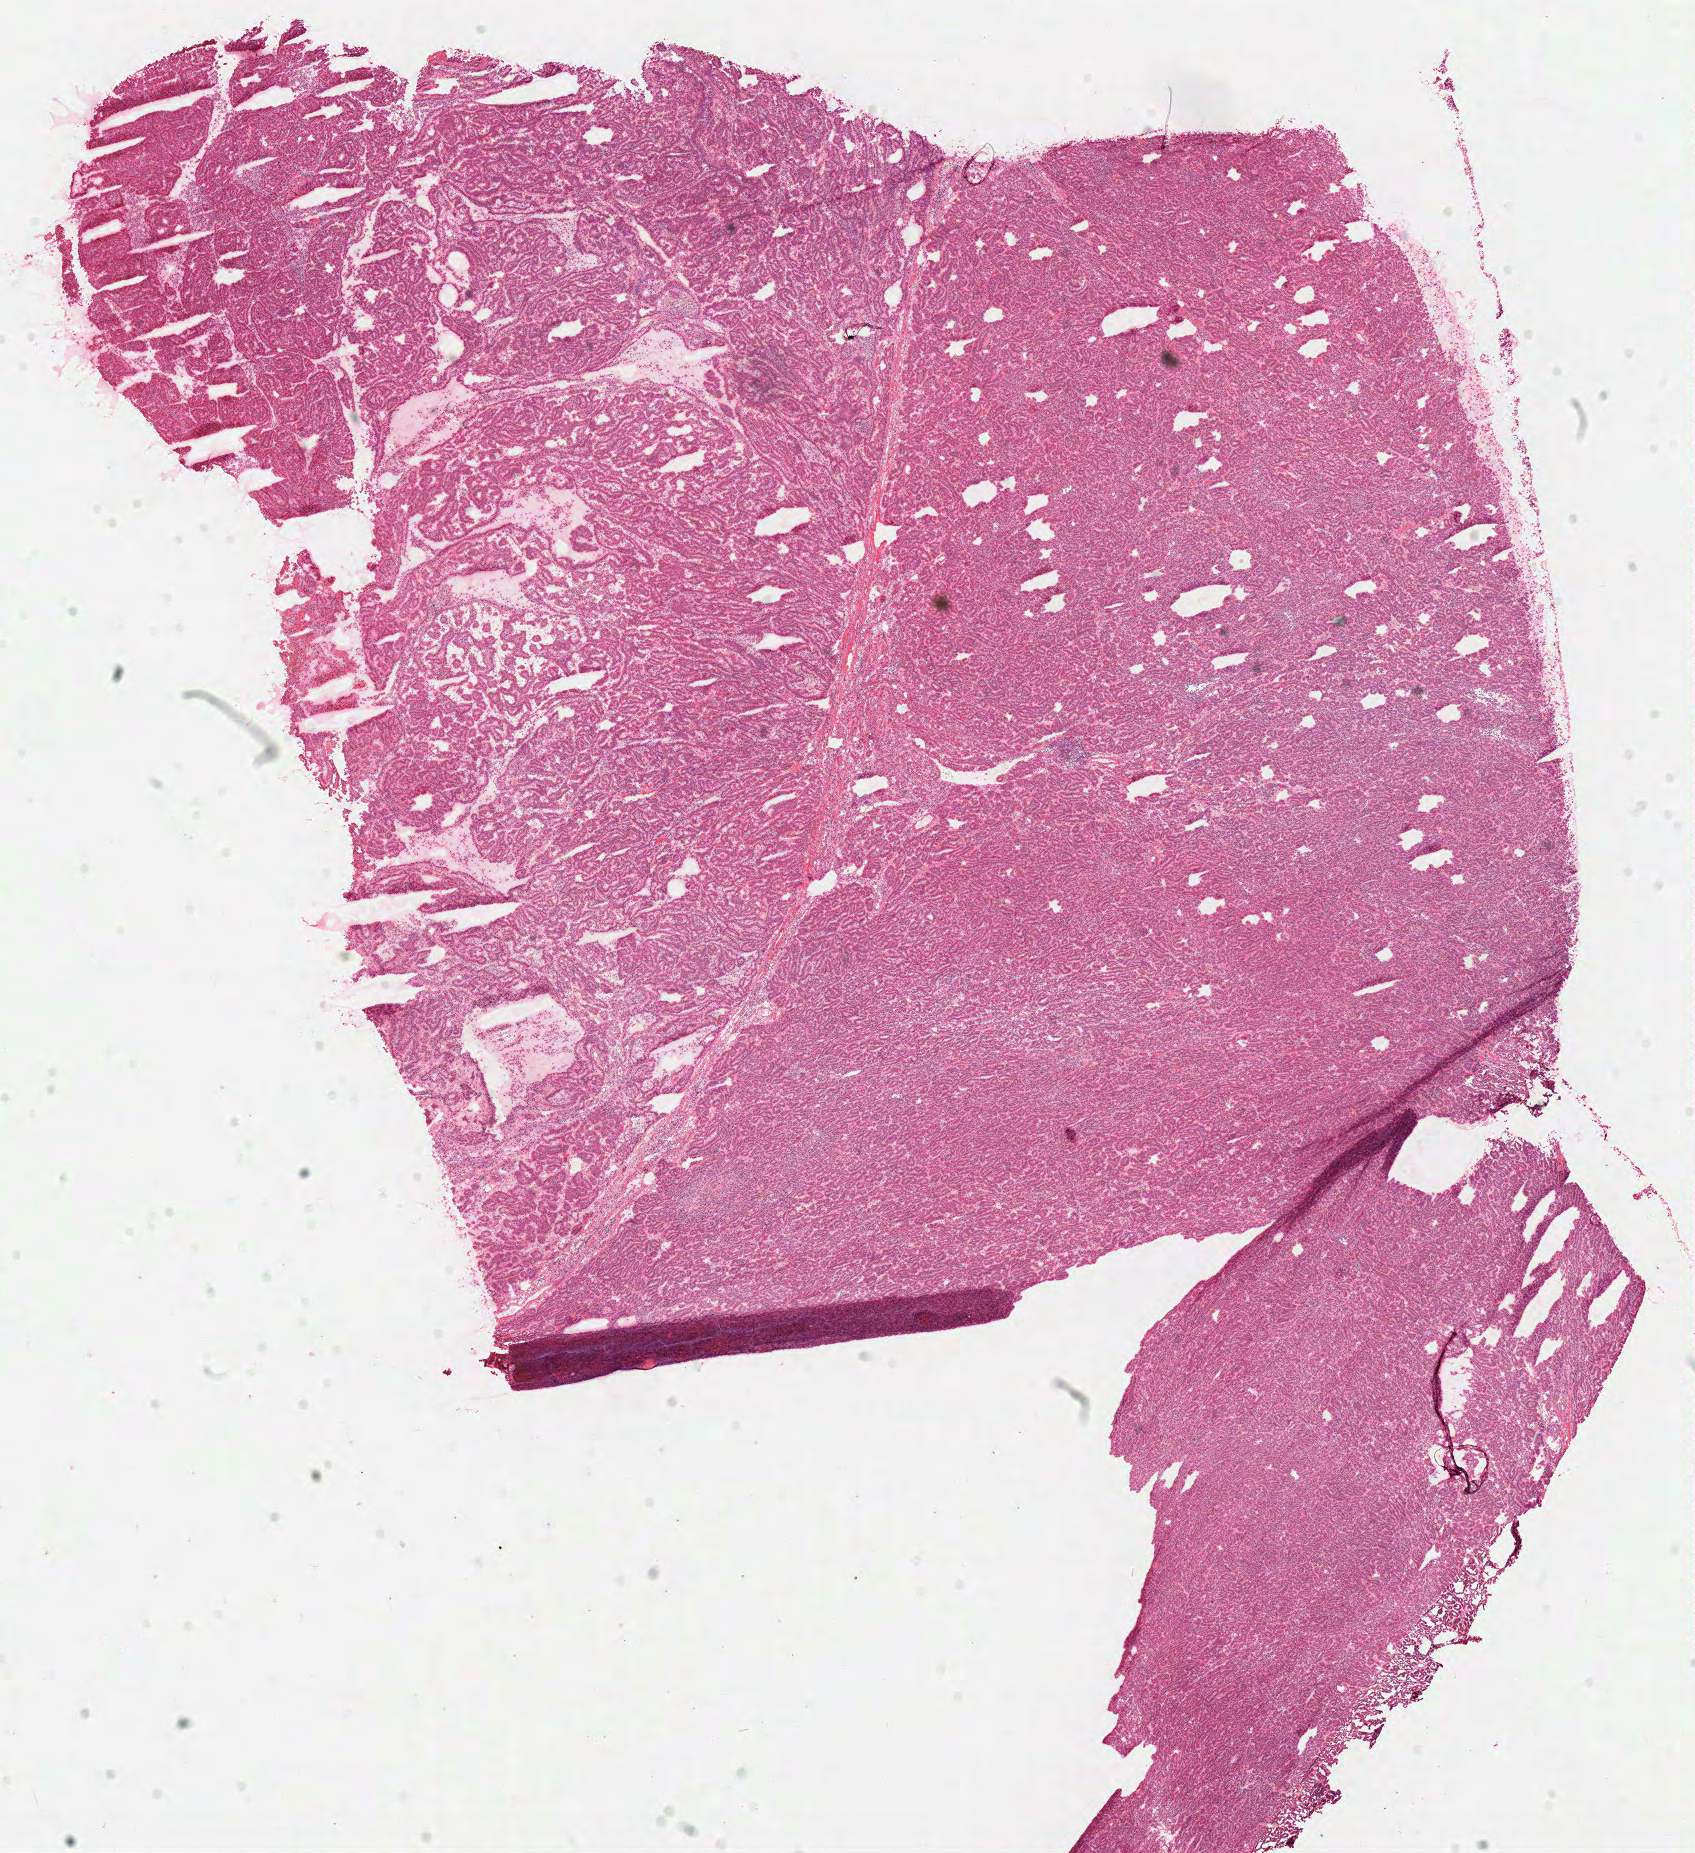
Whole-slide histology image, H&E — low-resolution overview of the scanned area, about 13.4 x 14.6 mm (acquisition: 40x scan). Frozen section from the top of the tissue portion. Primary tumour sample from the kidney. Male, age 63 years at initial diagnosis. Pathologist review of this section (percent, as recorded): tumour cells 95%, tumour nuclei 85%, normal cells 0%, stromal cells 5%, necrosis 0%.
Lymph nodes positive (case pathology): 0 of 15 examined. Histologic diagnosis: Papillary adenocarcinoma, NOS. Laterality: left. AJCC pathologic stage: III.